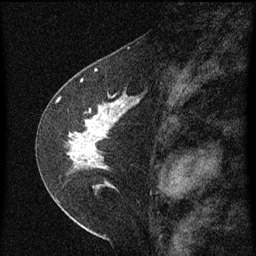
Breast MRI (dynamic contrast-enhanced), one sagittal slice; position 34 of 60 along the scan axis; dynamic contrast-enhanced series, image 2 of 3 at this slice position (ordered by acquisition); 1.5 T; TE 4.2 ms, TR 8 ms; 256 × 256 image matrix. Patient: female, 47 years.
Structures marked on this image (semi-automatically segmented with operator editing):
- analysis volume of interest (the breast-tissue region the enhancement analysis was run in; not a lesion): bounding box (x1, y1, x2, y2) in pixels: (44, 84, 147, 199)
- tumour enhancement mask (voxels above the 70 % enhancement threshold inside the analysis volume of interest): (68, 96, 127, 189)